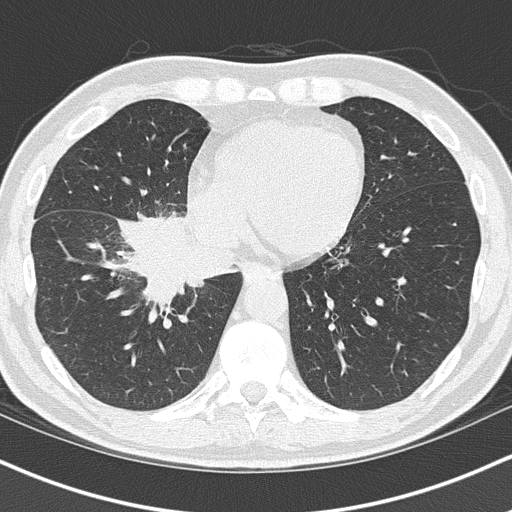
Chest CT (low-dose screening protocol), one axial image. First (baseline) screen. Lung window (W 1500 / L -600 HU). 2 mm slice thickness. Lung (sharp) reconstruction kernel (B50f). Male participant, aged 55 years at enrolment. Current smoker at enrolment.
- Expert reader's lesion annotation, box from (x=123, y=223) to (x=243, y=314) px.
- Screening reader's record for this exam (one nodule recorded; not confirmed to be the boxed lesion): non-calcified nodule or mass ≥4 mm, right lower lobe, 6 × 5 mm, spiculated (stellate) margins, soft tissue attenuation.
- Later outcome: lung cancer diagnosed 21 days after this screen — carcinoma, NOS, right hilum, stage IB (AJCC 6th edition), 67 mm at pathology.